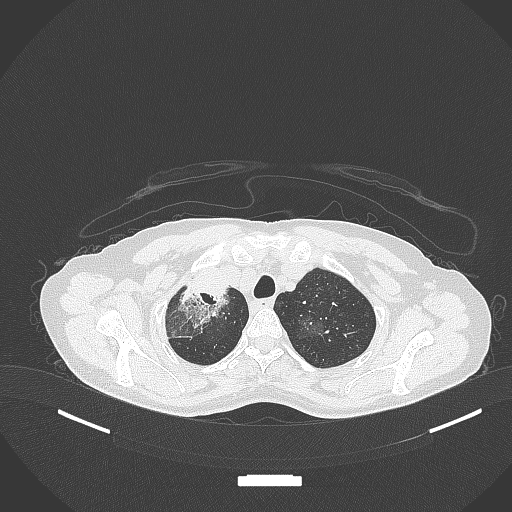
Chest CT, one axial slice; position 278 of 284 along the scan axis; 120 kVp; lung window (W 1500 / L -600 HU); 1 mm slice thickness; 512 × 512 image matrix. Female patient, age 59 years. Case-level facts recorded for this patient, not image findings: clinical TNM (as recorded): T3 N0 M0; histopathological grade: G1.
Outlined on this slice (rectangle marked by the reading radiologist):
- lung tumour (recorded histology: adenocarcinoma): box from (x=172, y=276) to (x=231, y=328) px